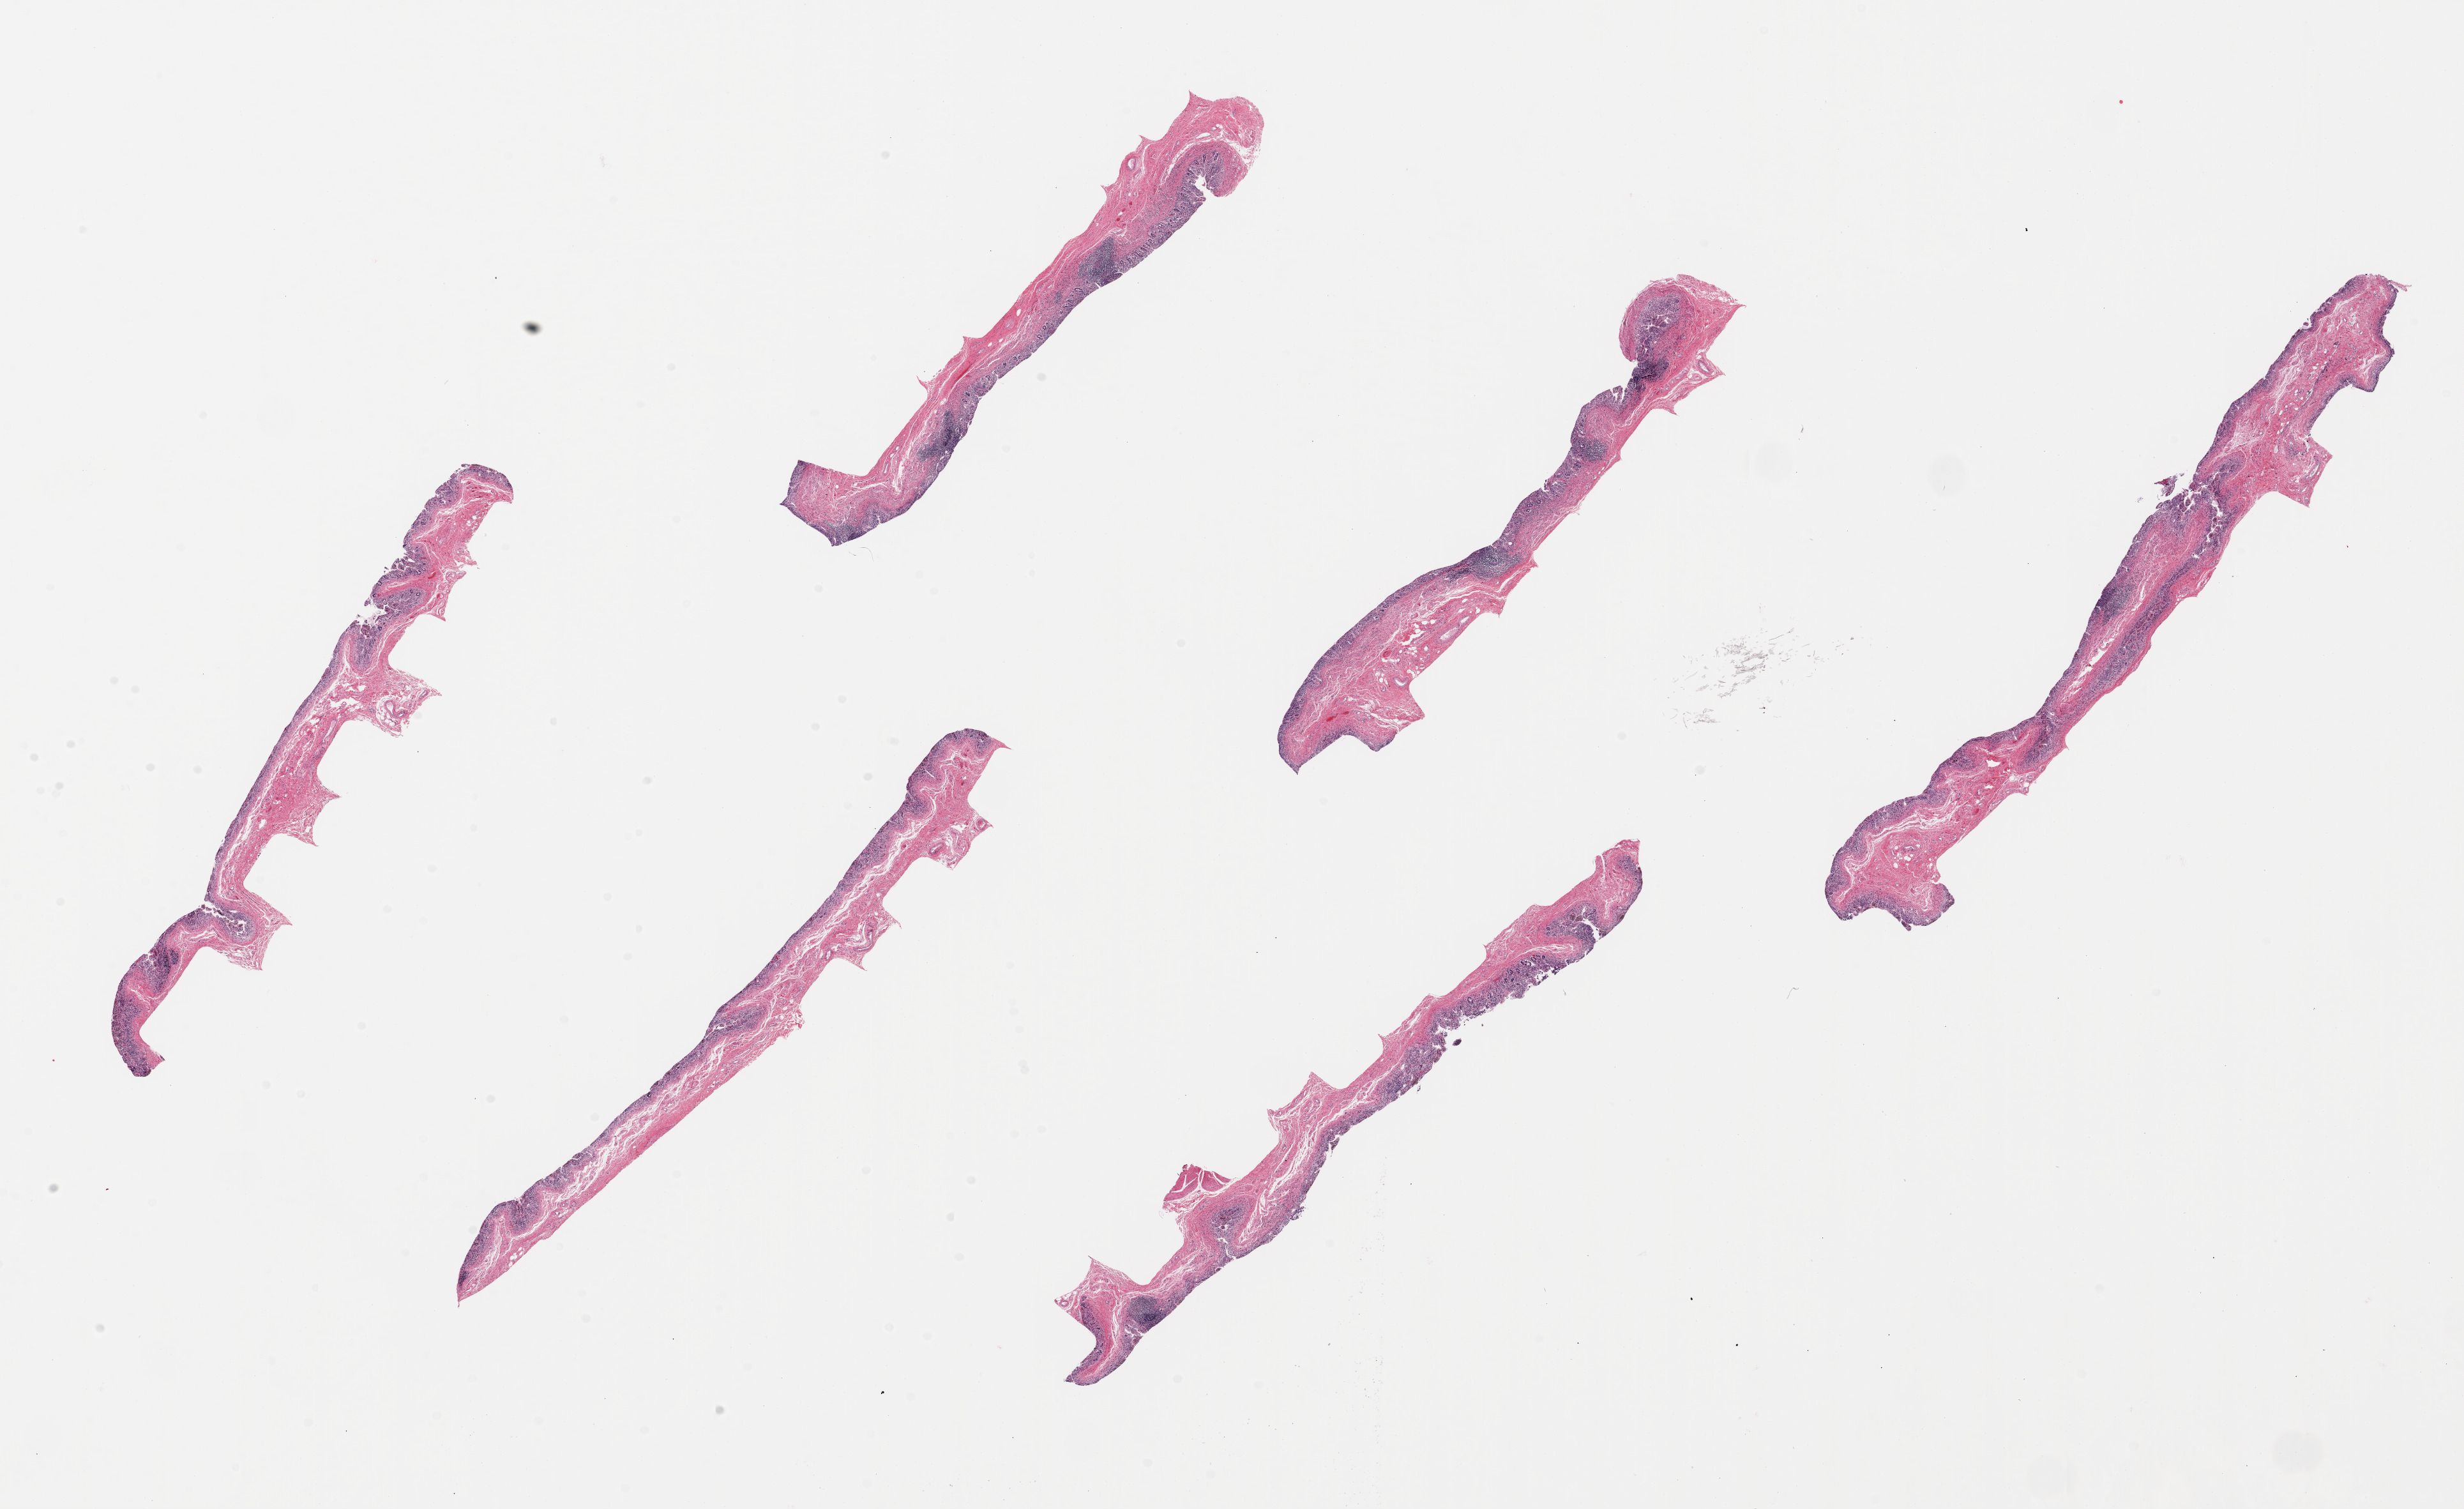
H&E whole-slide image — low-resolution overview of the scanned area, about 30.5 x 18.7 mm; PAXgene-fixed, paraffin-embedded tissue; target tissue: ileum; tissue donor sample. Donor: female.
Pathologist's review note for this sample: 6 pieces, up to 10.5x1.5mm; sparse lymphoid nodules, moderately autolyzed; totally autolyzed glands; mucosa and submucosa as targeted, no muscularis.